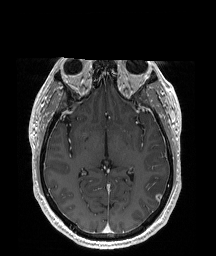
Brain MRI from a brain-tumour surgery series, one axial slice. Position 106 of 192 along the scan axis. T1-weighted post-contrast. 216 × 256 image matrix. From the clinical record (not read from this slice): histopathology: Glioblastoma; WHO grade: 4; IDH mutation: no; tumour location: Left Temporal Parietal.
Outlined on this slice (manually delineated by an expert):
- tumour: bounding box [x1, y1, x2, y2] px = [144, 175, 167, 202]